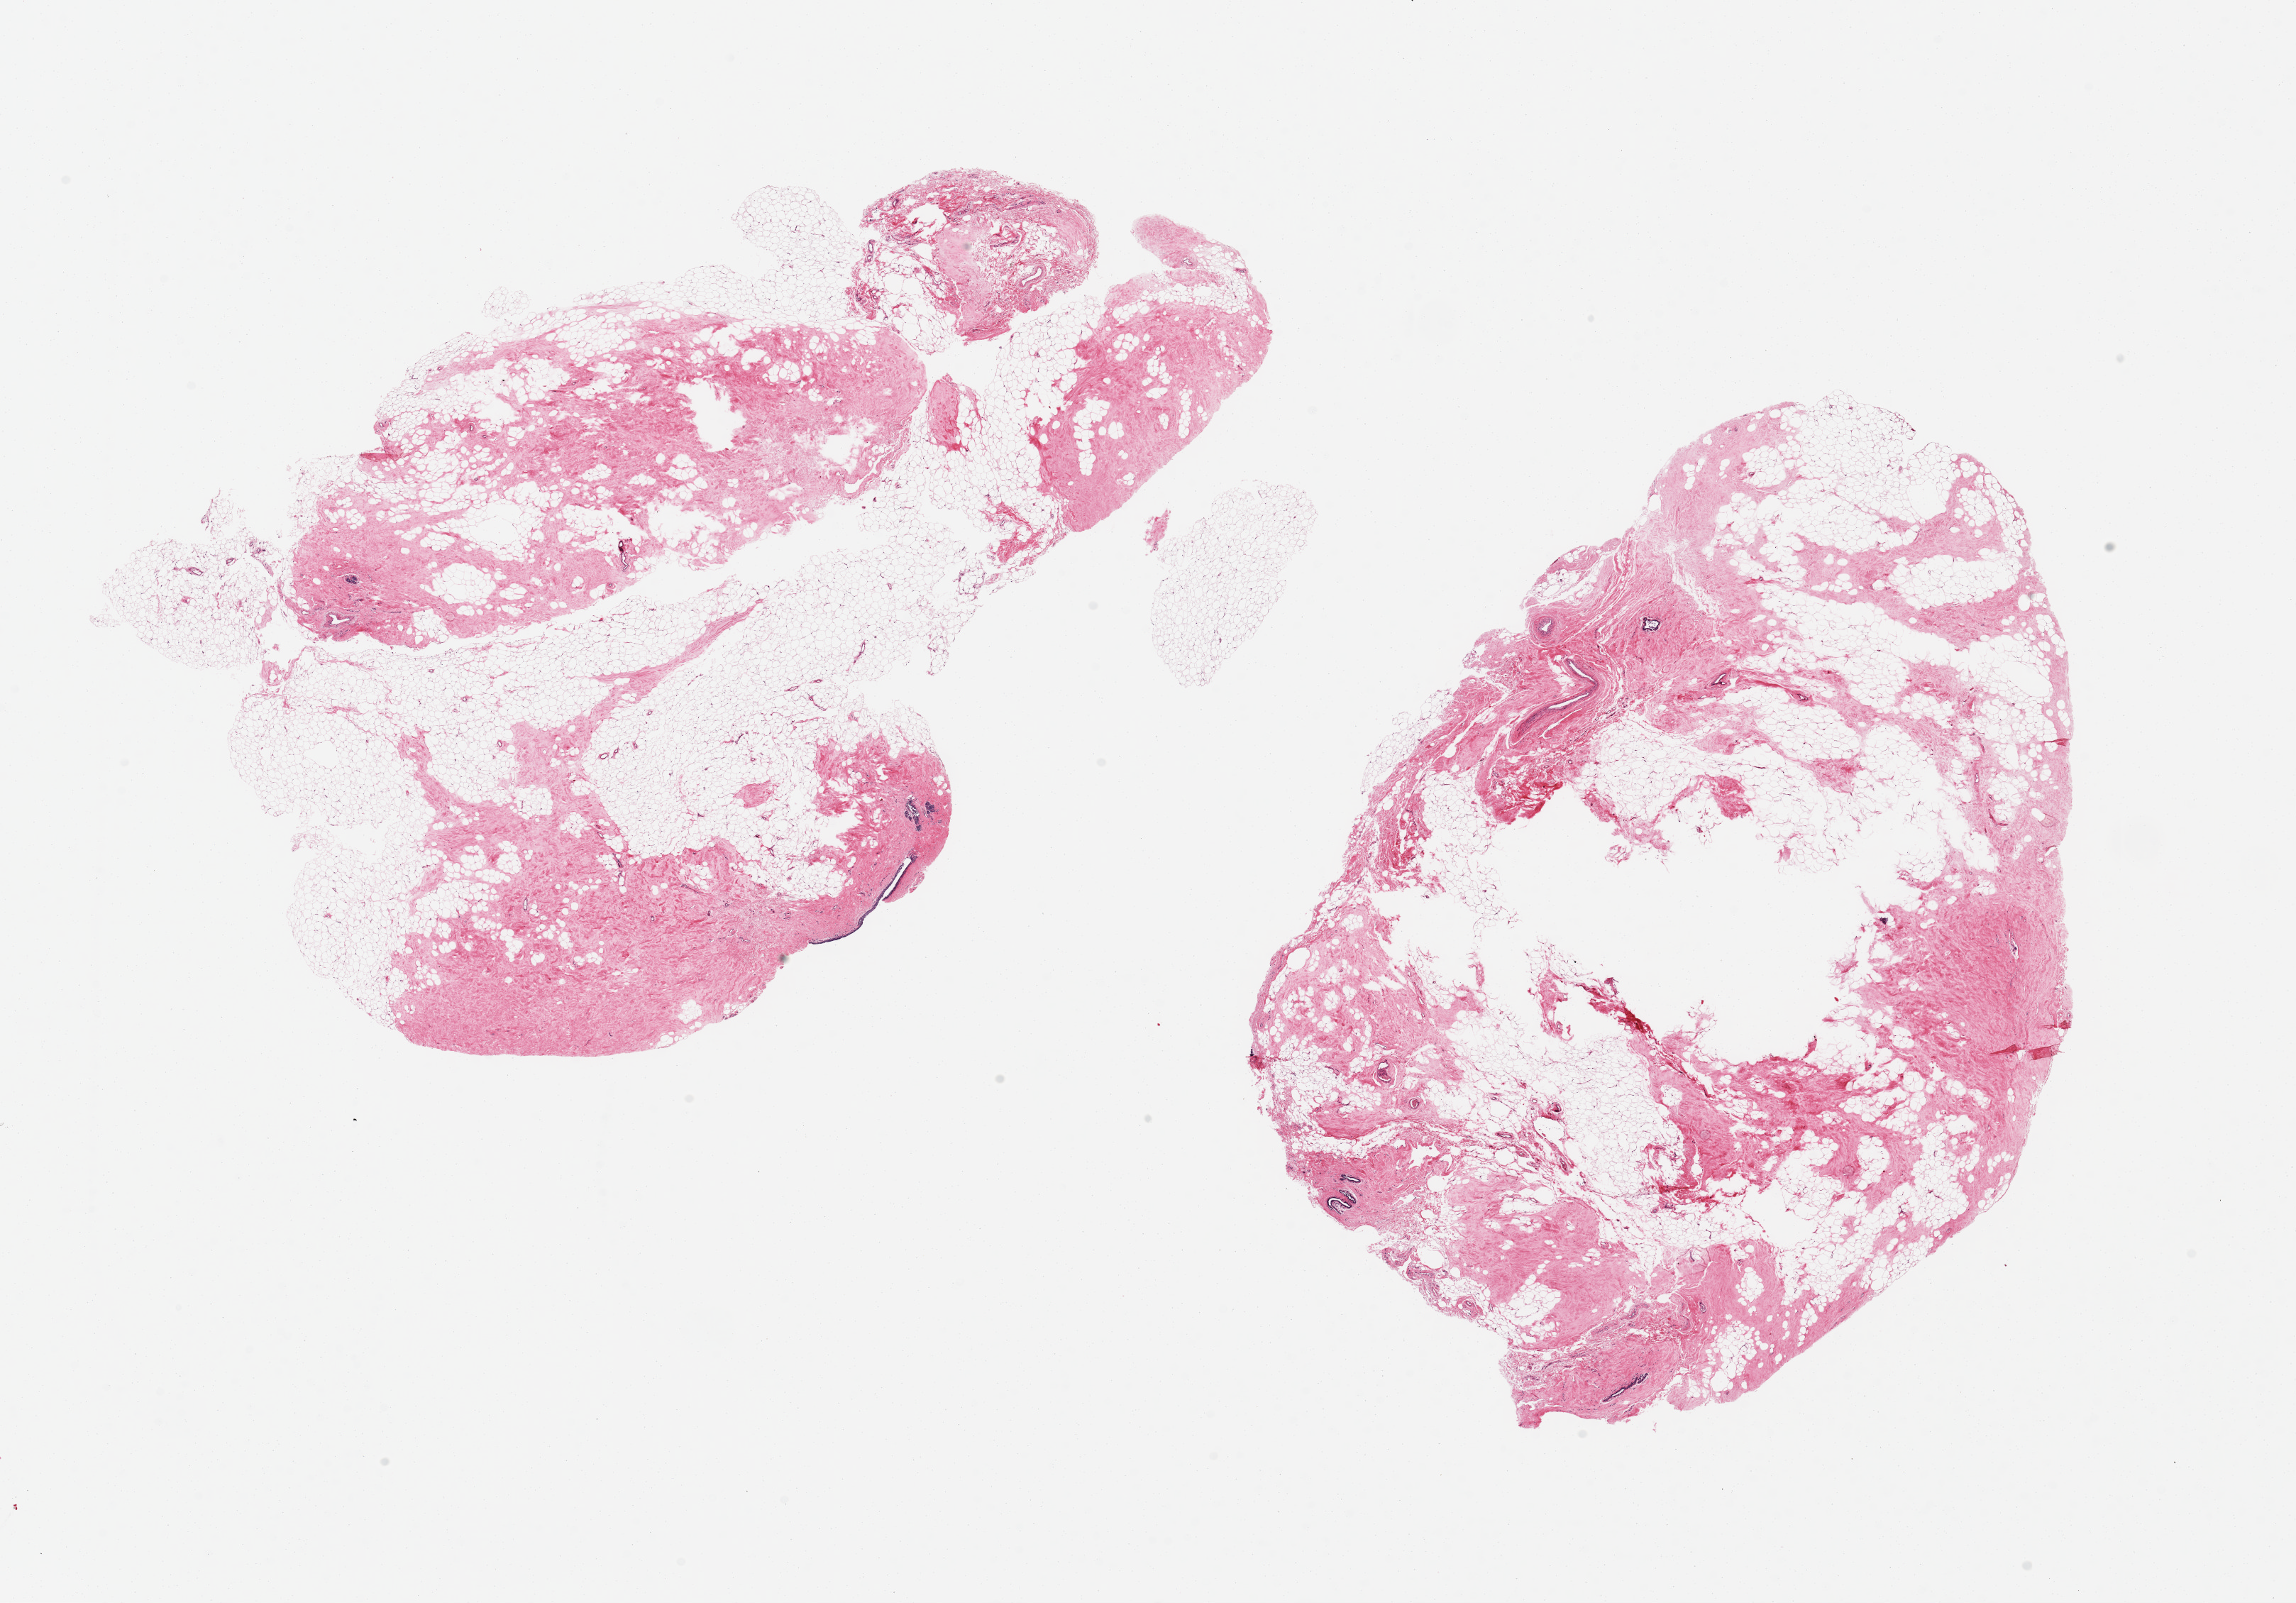
Whole-slide image, haematoxylin and eosin stain — low-resolution overview of the scanned area, about 25.6 x 17.9 mm, PAXgene-fixed paraffin-embedded (PFPE) section, target tissue: breast, tissue donor sample. Female donor.
Pathologist's review note for this sample: 2 aliquots, ~11x8mm. Rare minute foci of atrophic ductal elements.